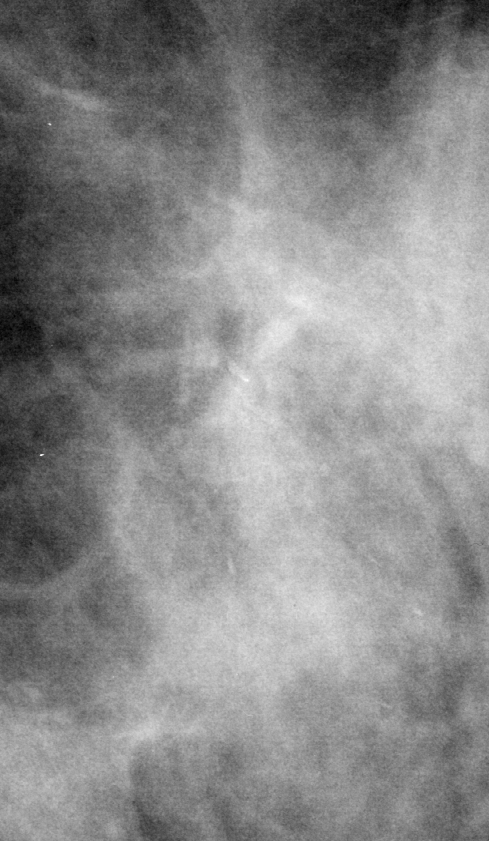
Cropped region of a digitized screen-film mammogram centred on a radiologist-marked abnormality; left breast; MLO view; BI-RADS breast density category 2 (scale 1–4).
- Marked abnormality: calcifications, morphology fine linear branching, distribution linear; BI-RADS assessment category 4; subtlety rating 4 on a 1 (subtle) to 5 (obvious) scale; pathology result (as recorded, not read from the image): benign.